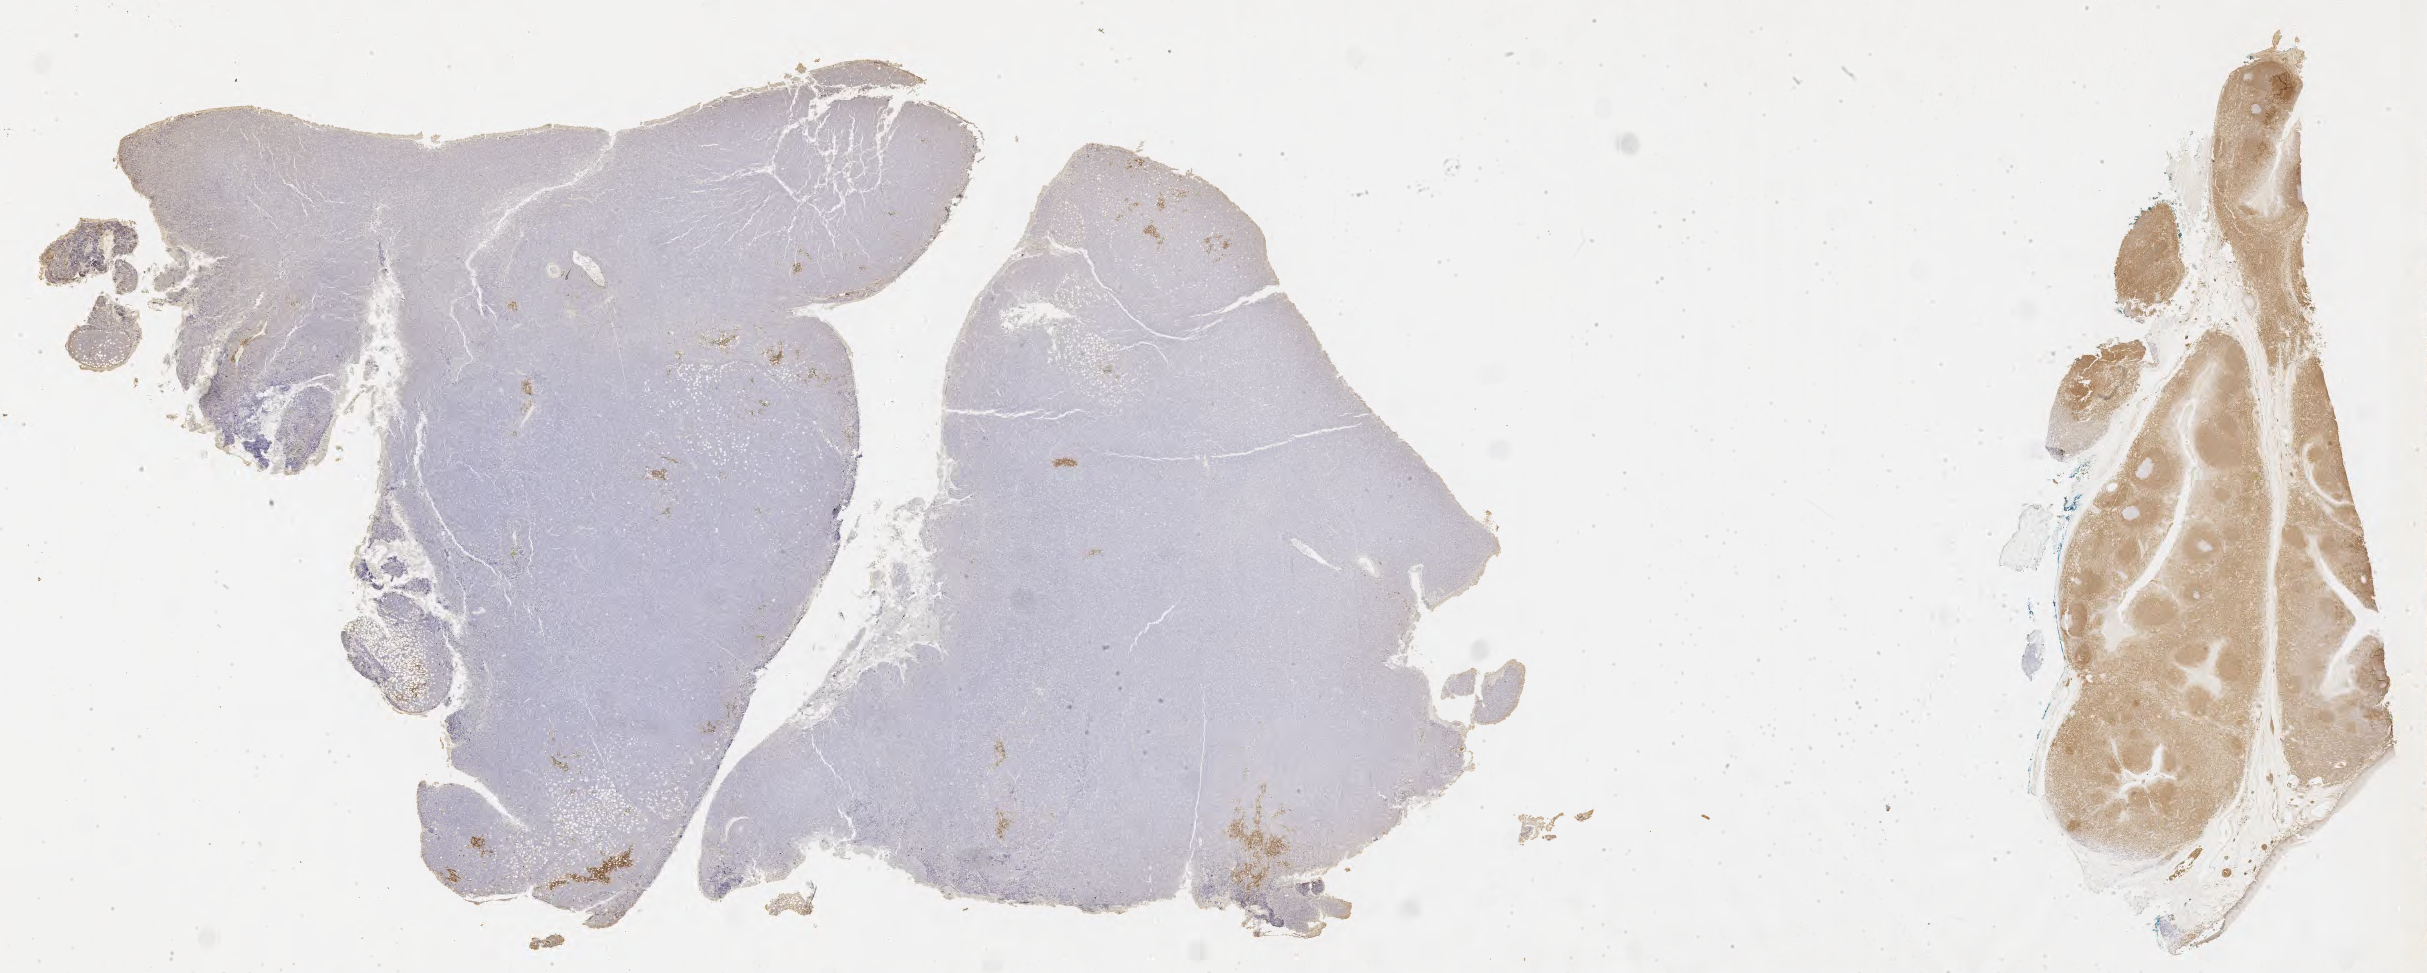
IHC for BCL2, whole-slide image — shown as a low-resolution overview of the whole scanned area (about 39.2 x 15.7 mm); specimen: tumor tissue; anatomic site: peritoneum. Patient: male, age at initial diagnosis 9 years.
• diagnosis: Burkitt lymphoma, NOS